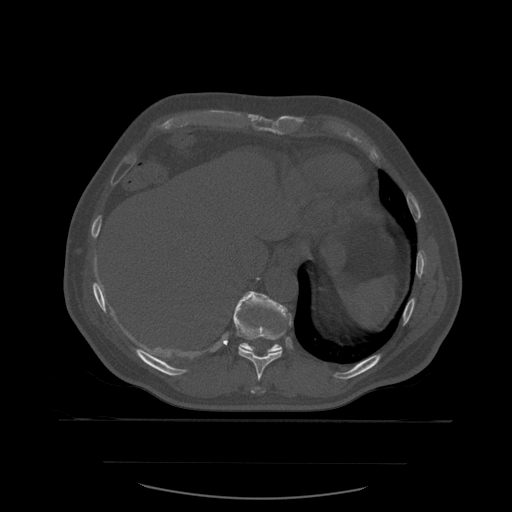
CT including the spine, one axial slice; slice 312 of 590 in the series (ordered by position); bone window (W 1800 / L 400 HU); 512 × 512 image matrix. Patient age 71 years. Case-level facts recorded for this patient, not image findings: primary cancer: lung.
Annotated regions visible in this slice (semi-automatically segmented with operator editing):
- T10 vertebra: bounding box <233,292,292,394> (left, top, right, bottom; pixels)
- T11 vertebra: <234,292,293,353>
- T9 vertebra: <251,388,266,394>